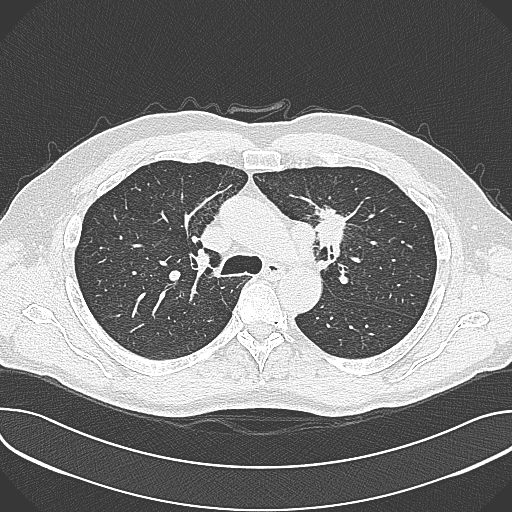
Chest CT (low-dose screening protocol), one axial image, baseline screening round, lung window (W 1500 / L -600 HU), 120 kVp. Male, age 59 years at enrolment.
- Expert reader's lesion annotation, bounding box <302,196,362,257> (left, top, right, bottom; pixels).
- The screening reader recorded 2 non-calcified nodules or masses ≥4 mm on this exam (left upper lobe, left upper lobe); which of them this box marks is not recorded.
- Official screen result: positive, change unspecified: nodule(s) >= 4 mm or enlarging nodule(s), mass(es), or other non-specific abnormalities suspicious for lung cancer.
- Lung cancer was diagnosed 21 days after this screen: non-small cell carcinoma, left upper lobe, poorly differentiated (G3), stage IIIA (AJCC 6th edition), 35 mm at pathology.